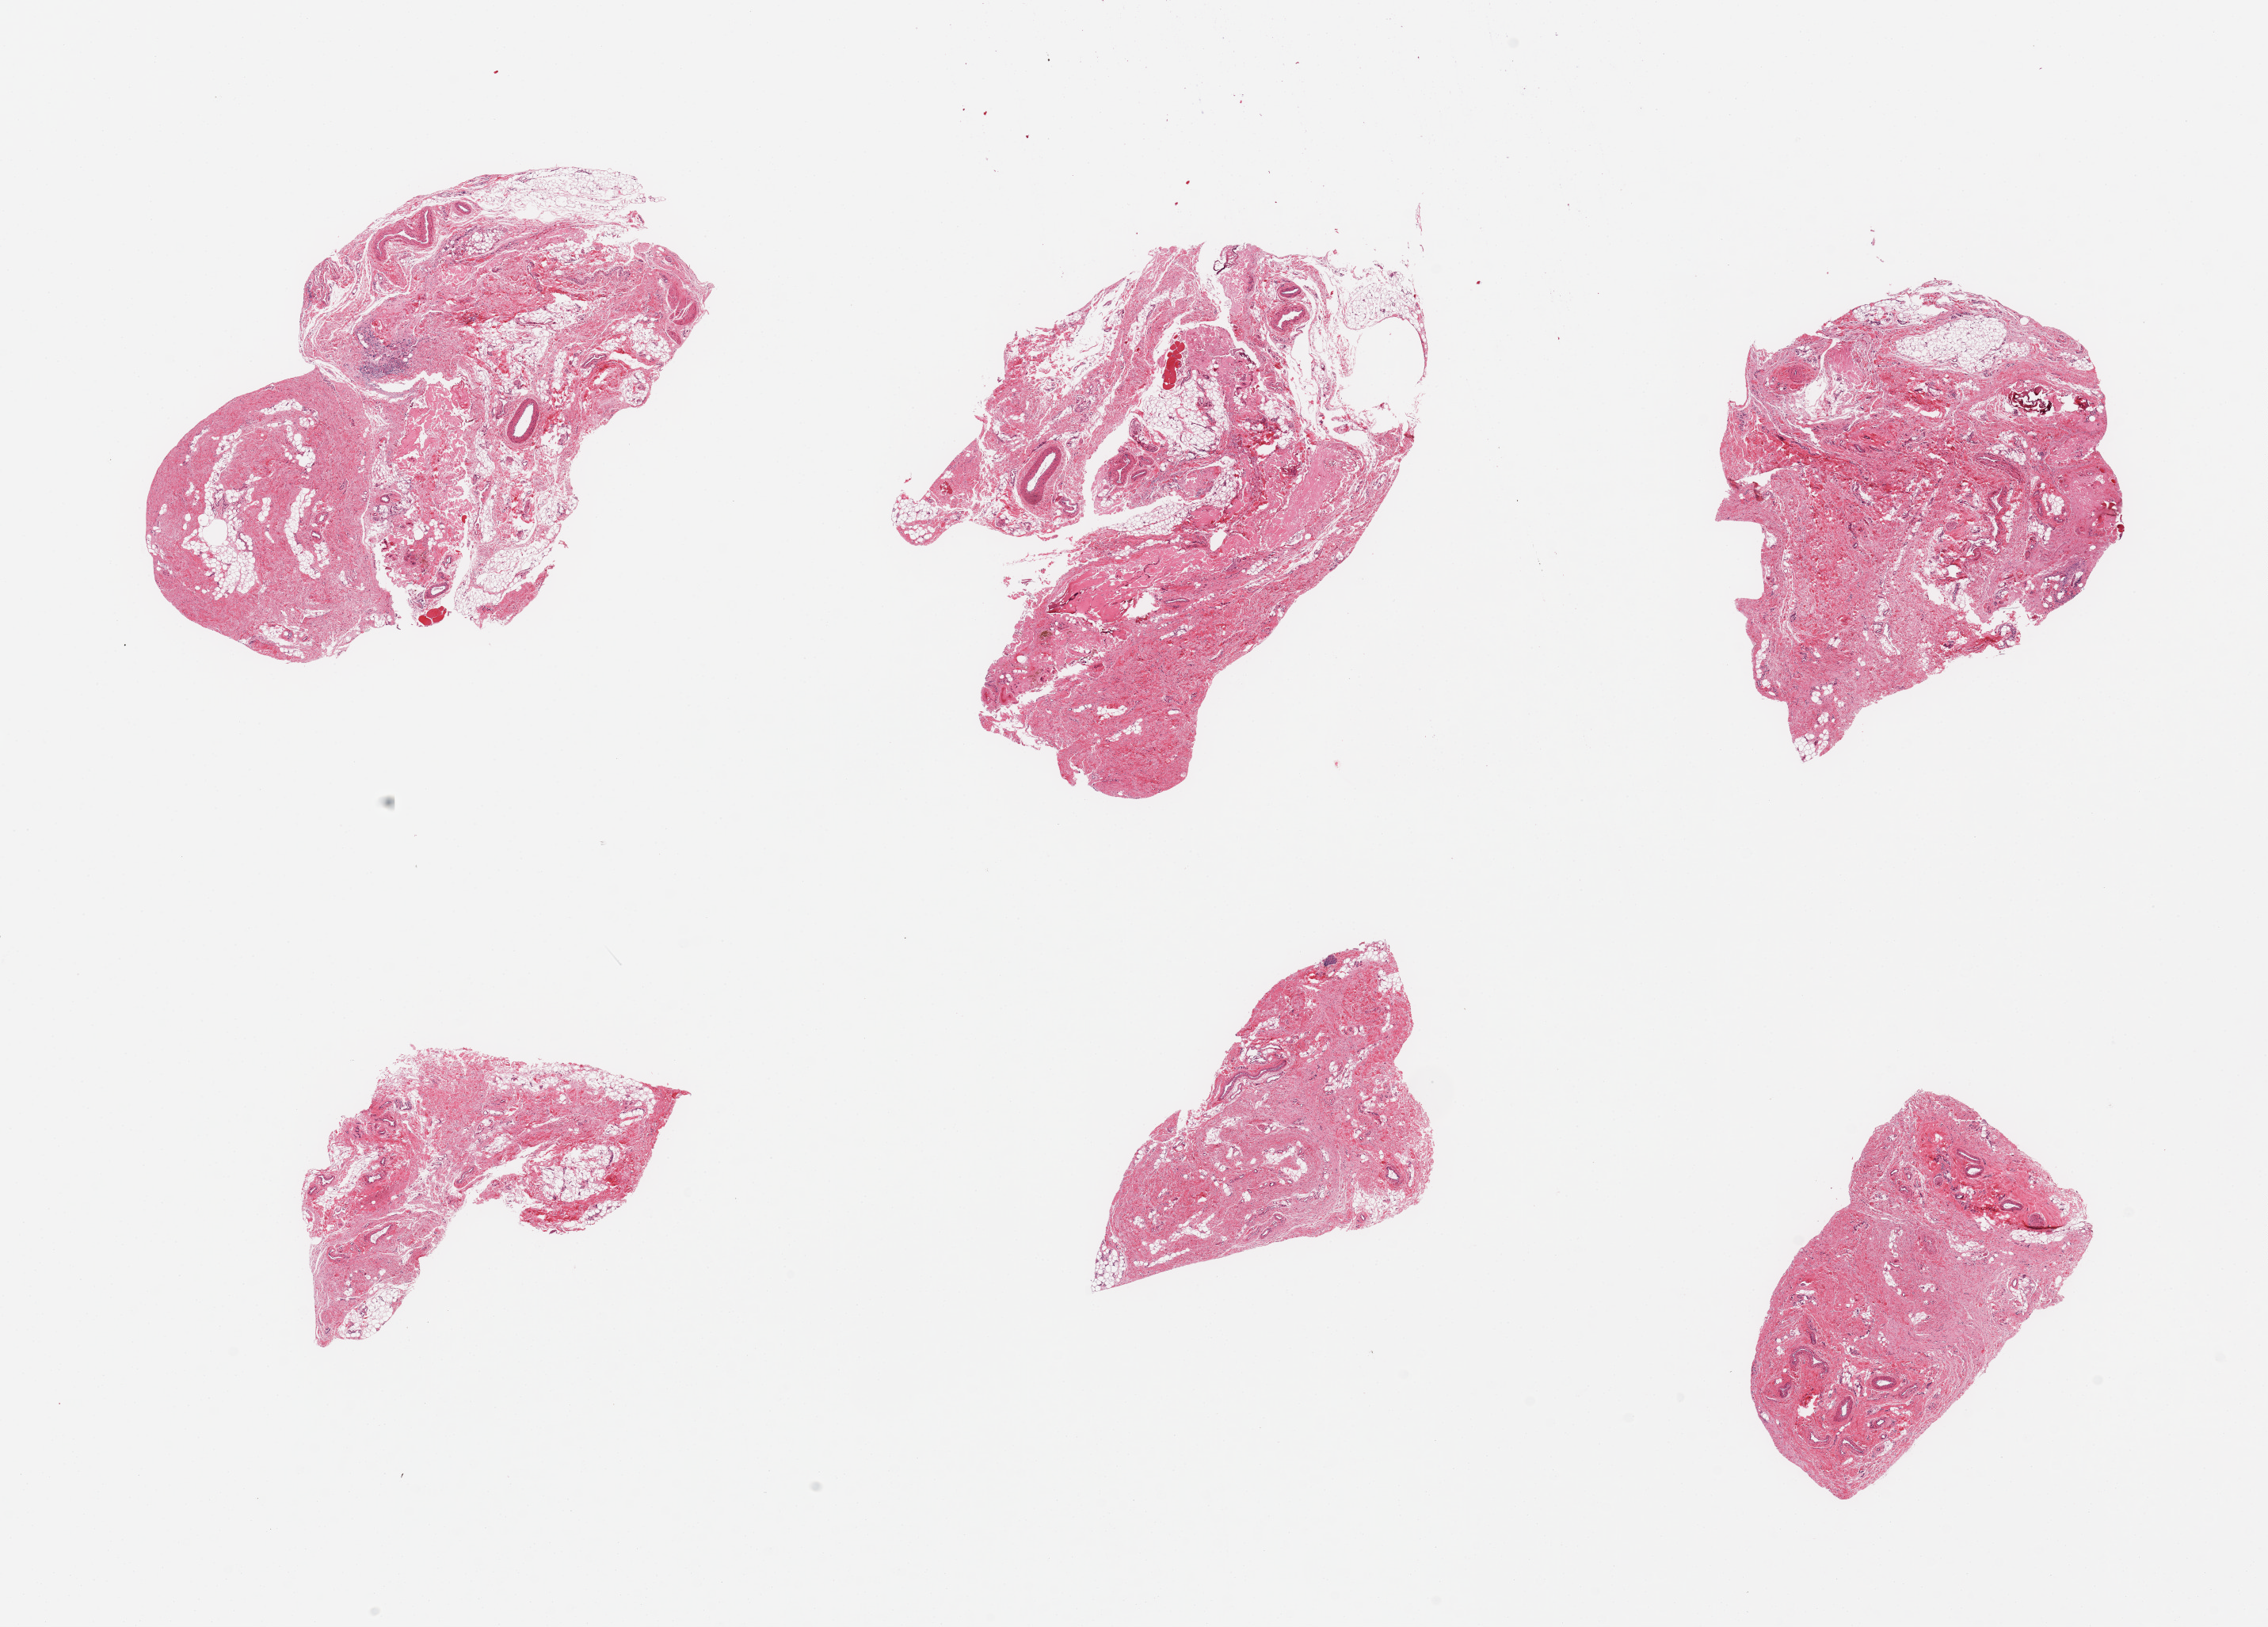
Digitized H&E-stained section — whole scanned area (about 22.6 x 16.2 mm) shown as a low-resolution overview. PAXgene-fixed paraffin-embedded (PFPE) section. Section of gastroesophageal junction (target tissue). Donor tissue sample. Donor: male.
Review note (as recorded): 6 pieces; predominantly submucosa.